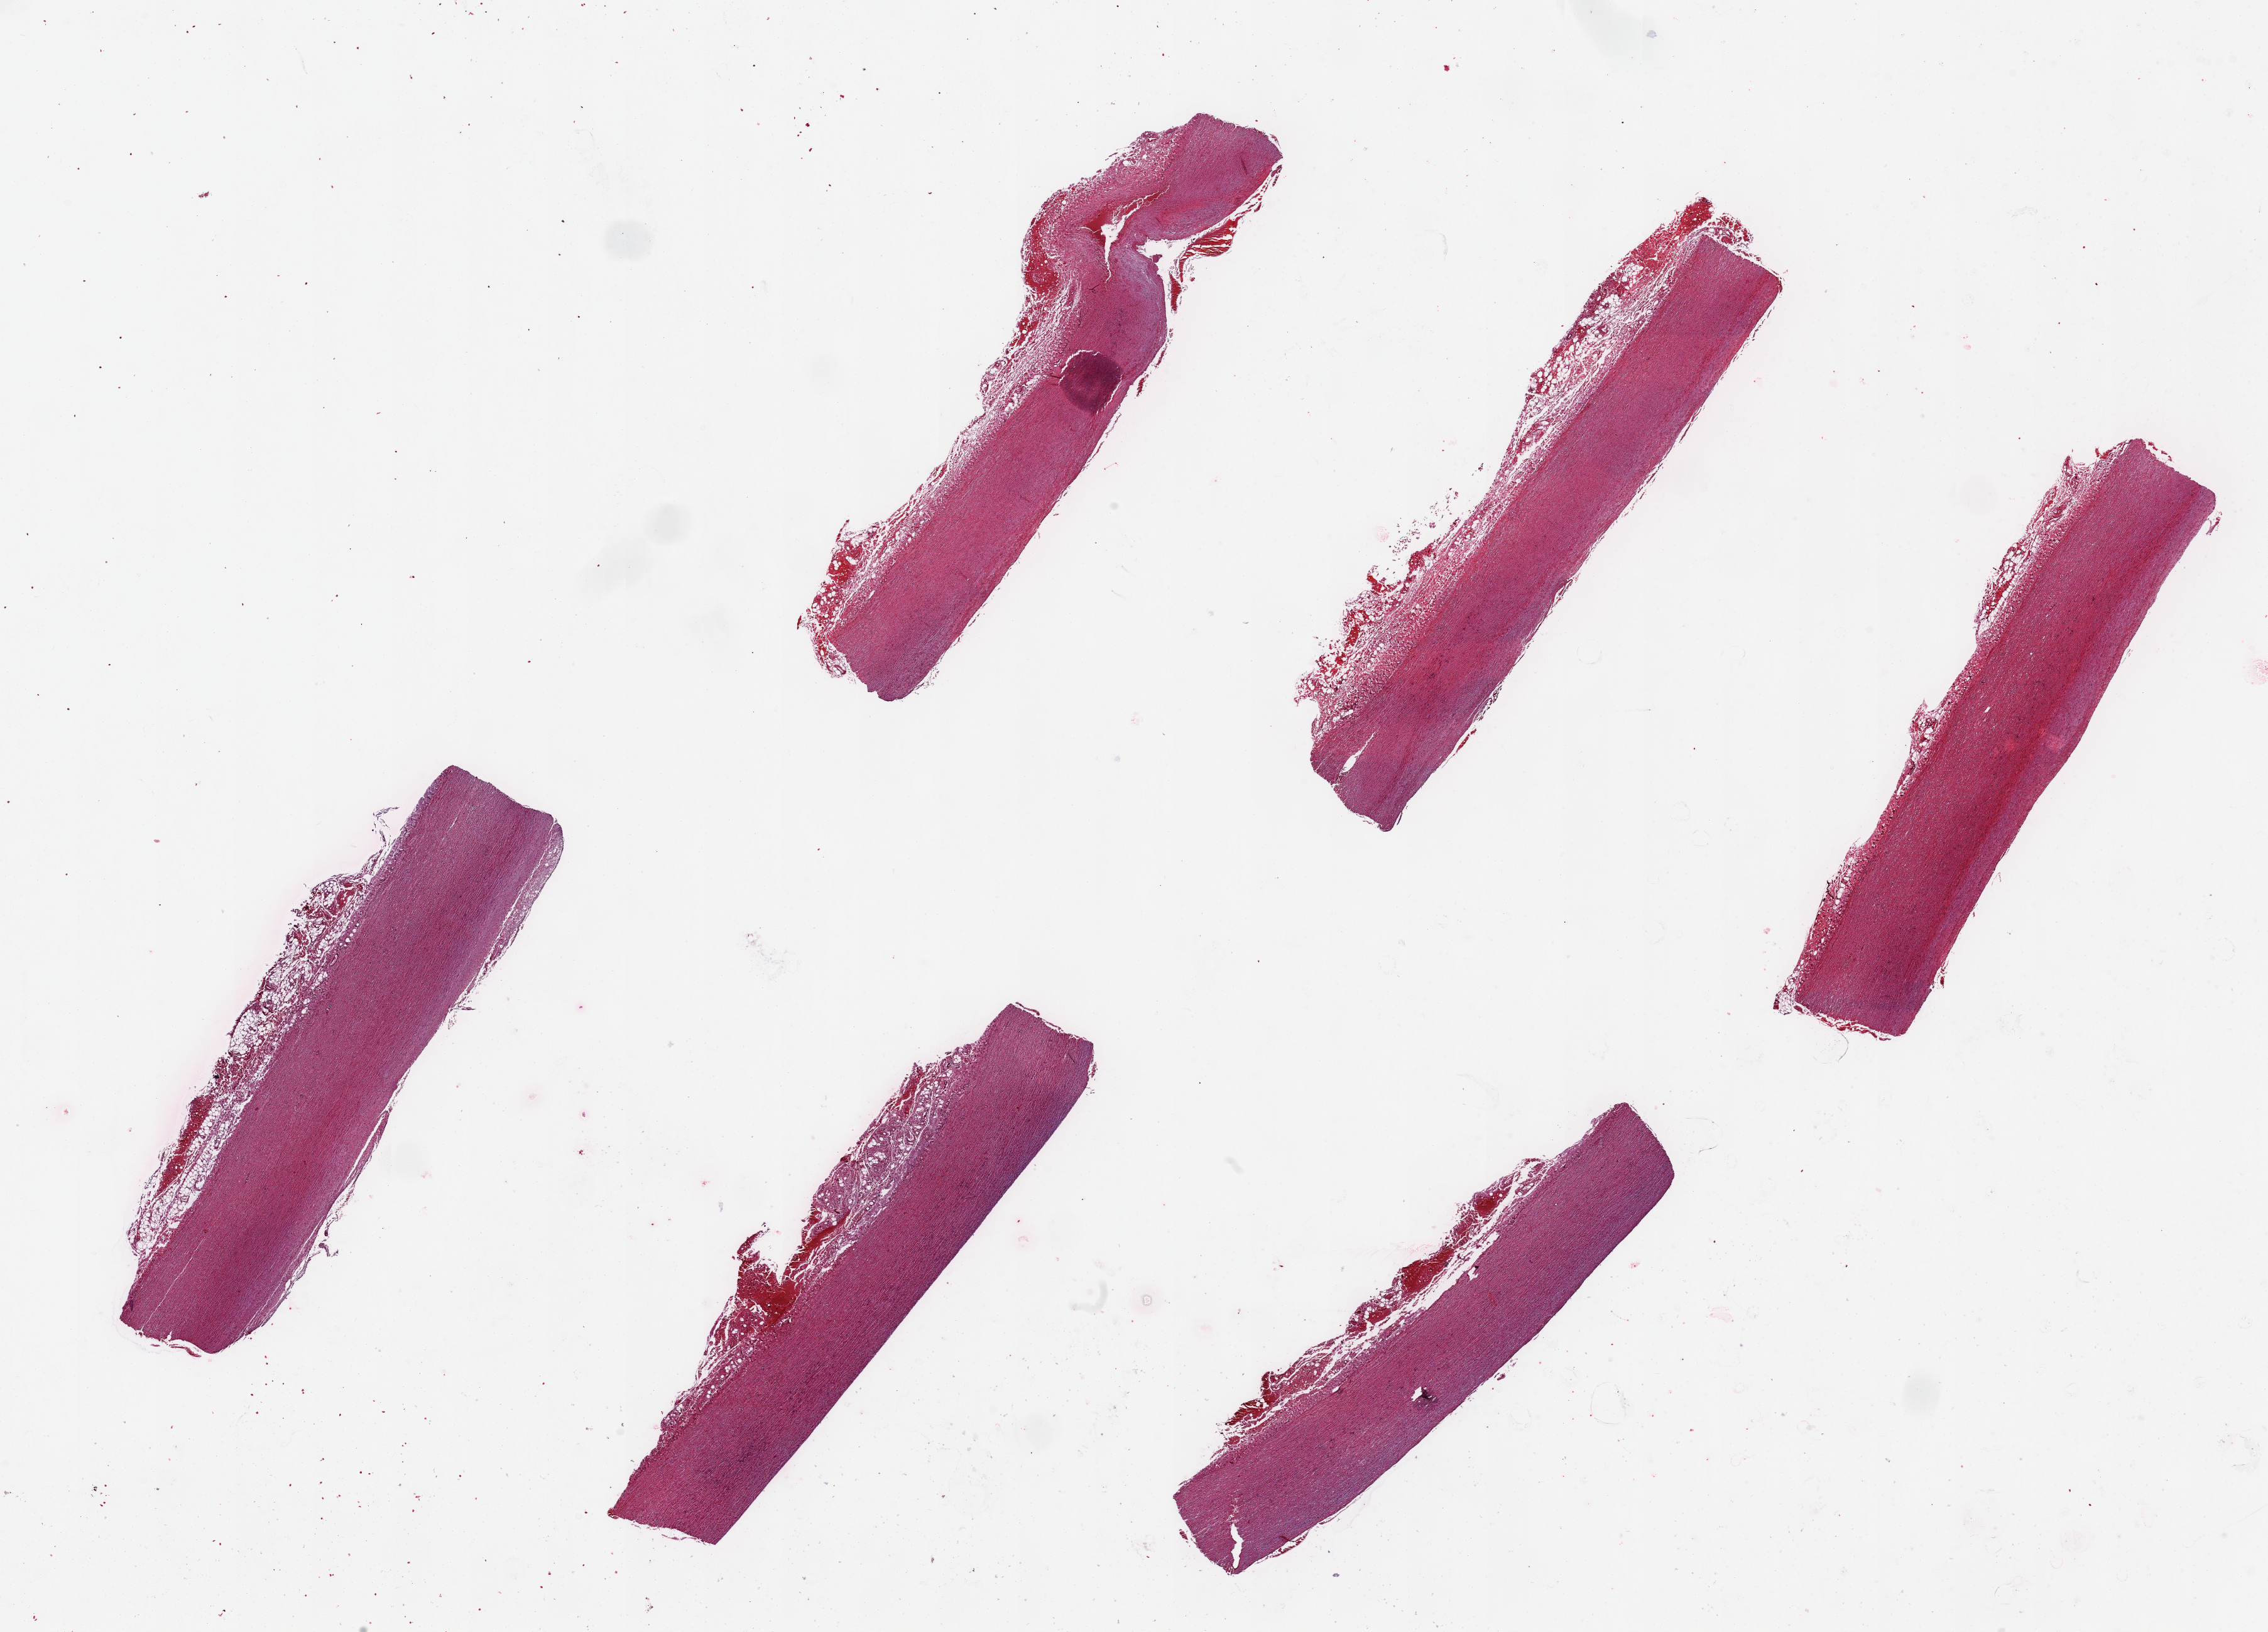
Haematoxylin and eosin whole-slide image — shown as a low-resolution overview of the whole scanned area (about 28.5 x 20.5 mm), PAXgene-fixed paraffin-embedded (PFPE) section, sampled site (target tissue): aorta, donor tissue sample. Donor: male.
- reviewer comment on this tissue sample: 6 pieces up to 9x2 mm; focal plaque and small dissection